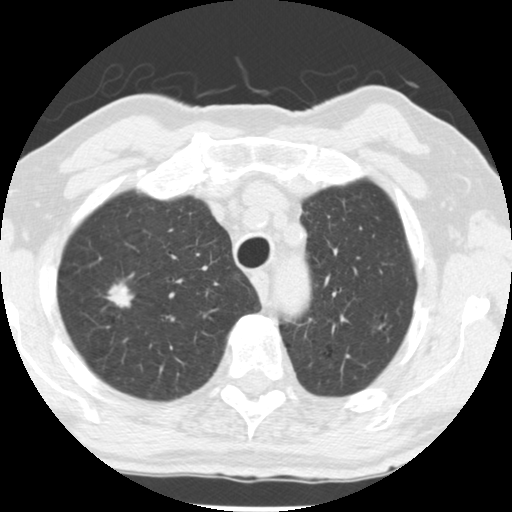
Axial slice from a low-dose chest CT screening exam. Baseline screening round. Lung window (W 1500 / L -600 HU). Slice 204 of 252 in the series. Male, age 69 years at enrolment. Former smoker at enrolment.
Expert-annotated lung lesion, bounding box [x1, y1, x2, y2] px = [91, 270, 150, 327]. The screening reader recorded 2 non-calcified nodules or masses ≥4 mm on this exam; which of them this box marks is not recorded. Official screen result: positive, change unspecified: nodule(s) >= 4 mm or enlarging nodule(s), mass(es), or other non-specific abnormalities suspicious for lung cancer. Later outcome: lung cancer diagnosed 105 days after this screen — adenocarcinoma, NOS, right upper lobe, well differentiated (G1), stage IA (AJCC 6th edition), 17 mm at pathology.